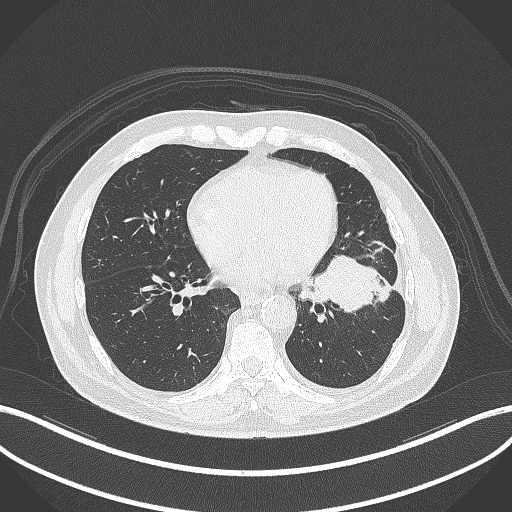
Chest CT, one axial slice; slice 143 of 230 in the series (ordered by position); reconstruction kernel B70f; lung window (W 1500 / L -600 HU); 1 mm slice thickness; 512 × 512 image matrix, field of view 400 × 400 mm. Male patient, age 68 years. From the clinical record (not read from this slice): clinical TNM (as recorded): T2b N0 M0.
Annotated regions visible in this slice (rectangle marked by the reading radiologist):
- lung tumour (recorded histology: squamous cell carcinoma): bounding box <311,247,395,317> (left, top, right, bottom; pixels)